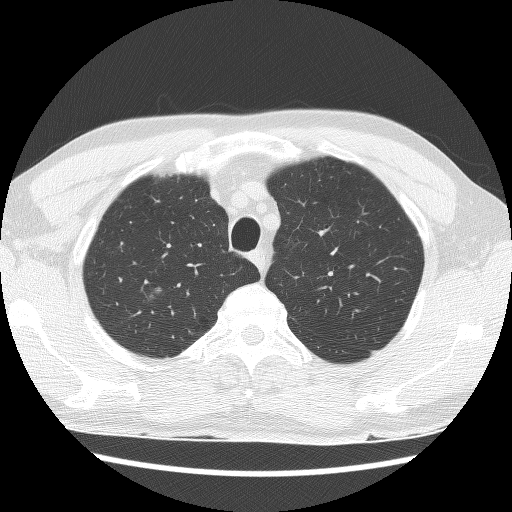
Low-dose screening chest CT, one axial slice. Slice 127 of 157 in the series (ordered by position). Lung window (W 1500 / L -600 HU). 512 × 512 image matrix, field of view 340 × 340 mm.
Annotated regions visible in this slice (manually delineated by an expert):
- lesion 1 (tumor, upper lobe of right lung): box from (x=150, y=287) to (x=162, y=298) px